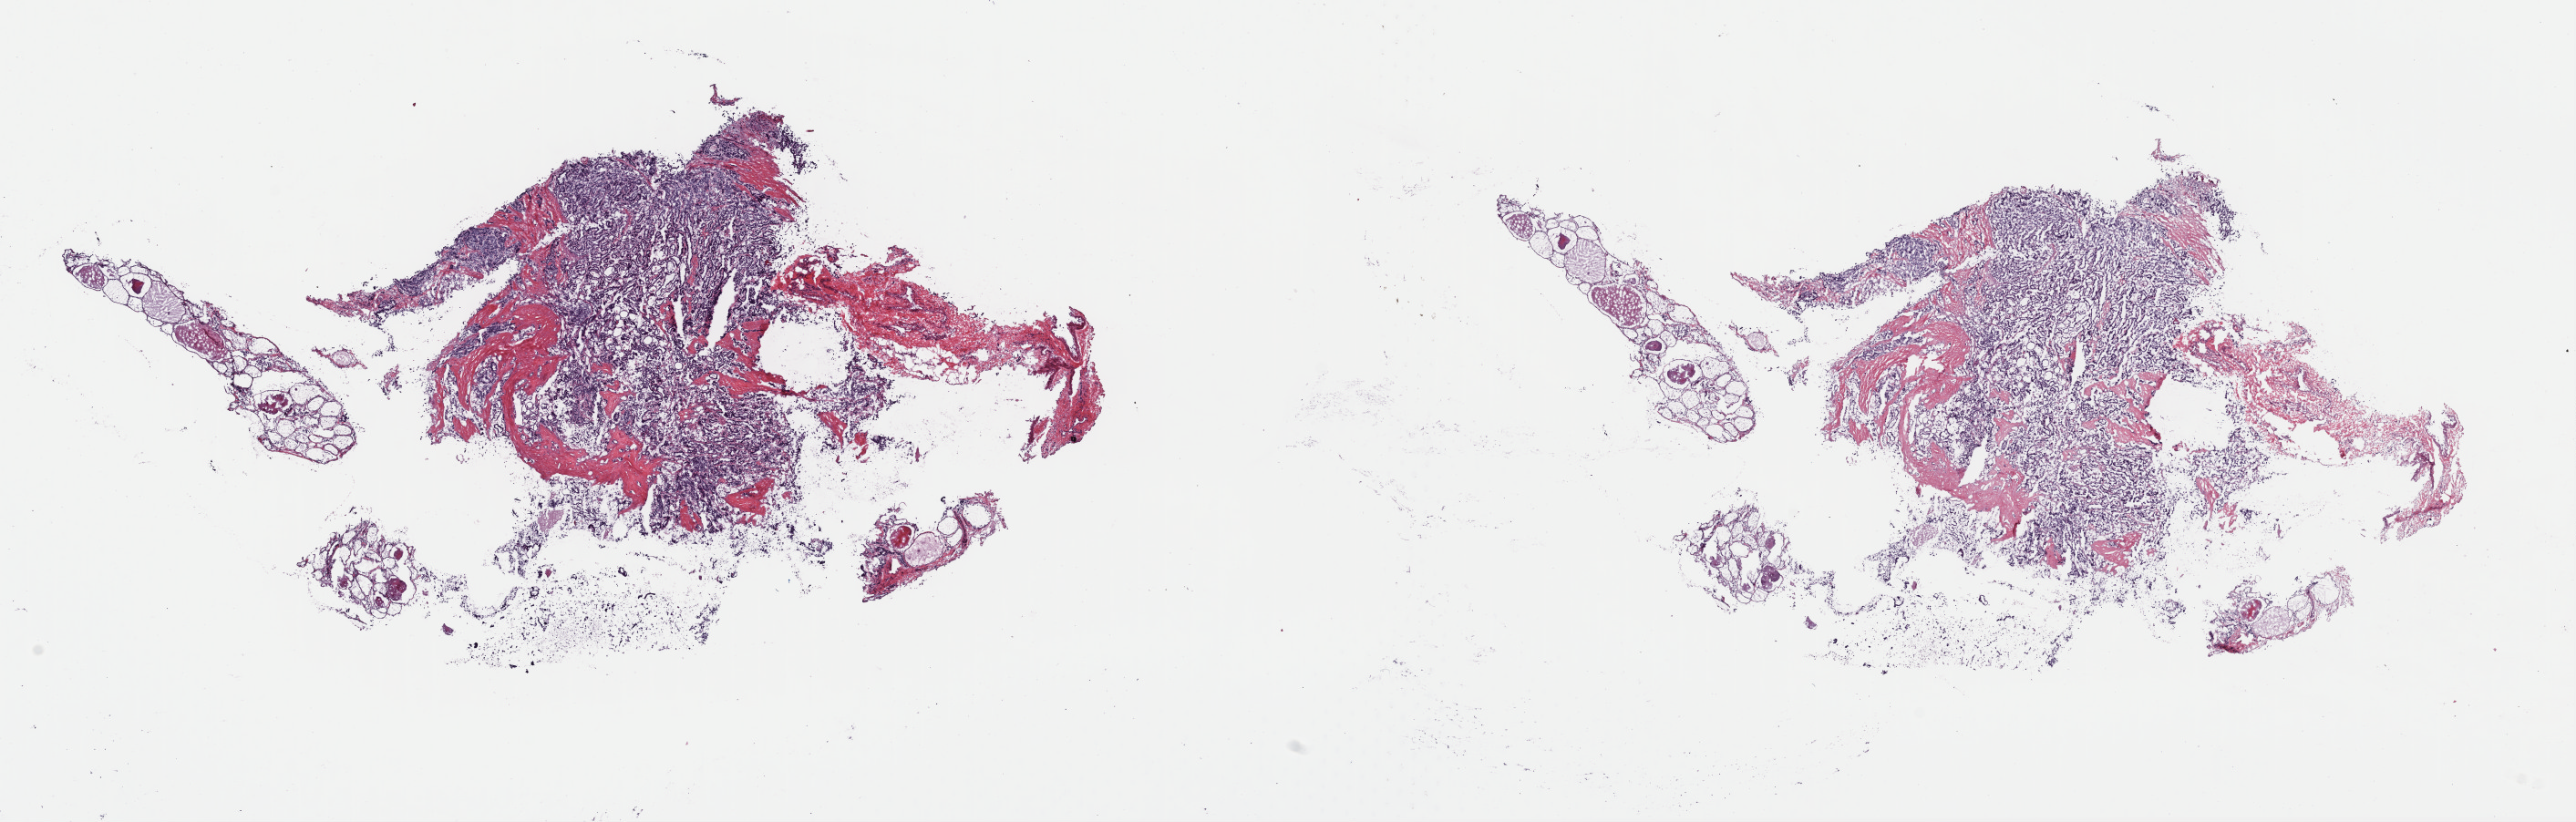
Hematoxylin and eosin (H&E) stained whole-slide image — low-resolution overview of the scanned area, about 22.3 x 7.1 mm. Frozen section from the top of the tissue portion. Thyroid, primary tumour sample. Female, age 34 years at initial diagnosis. Composition of this section per pathologist review: tumour cells 75%, tumour nuclei 75%, normal cells 0%, stromal cells 25%, necrosis 0%. Inflammatory infiltration, as recorded: lymphocyte infiltration 2%, monocyte infiltration 1%, neutrophil infiltration 1%.
Histologic diagnosis: Papillary carcinoma, columnar cell. AJCC pathologic stage: I.